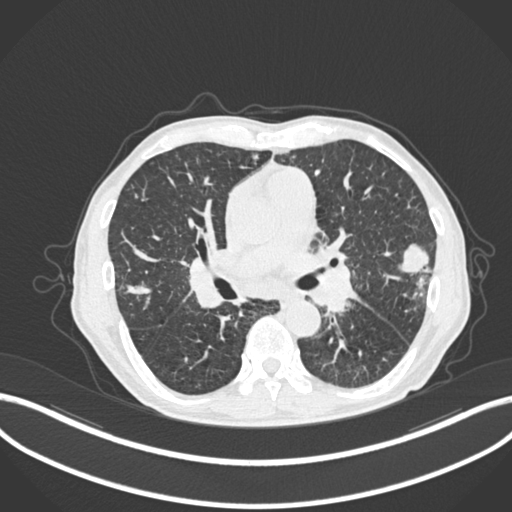
Chest CT, one axial slice. Position 125 of 287 along the scan axis. 120 kVp. Lung window (W 1500 / L -600 HU). 512 × 512 image matrix. Patient: male, 74 years. From the clinical record (not read from this slice): clinical TNM (as recorded): T2a N1 M0.
Outlined on this slice (bounding box drawn by a radiologist):
- lung tumour (recorded histology: adenocarcinoma): bounding box (x1, y1, x2, y2) in pixels: (400, 238, 430, 275)